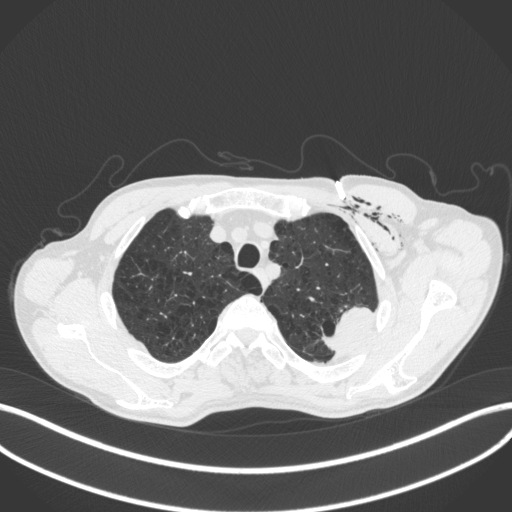
Chest CT, one axial slice. Position 345 of 416 along the scan axis. Reconstruction kernel B31f. 120 kVp. Lung window (W 1500 / L -600 HU). 1 mm slice thickness. 512 × 512 image matrix, field of view 400 × 400 mm. Patient: male, 58 years. From the clinical record (not read from this slice): clinical TNM (as recorded): T3 N0 M0.
Outlined on this slice (bounding box drawn by a radiologist):
- lung tumour (recorded histology: adenocarcinoma): bounding box (x1, y1, x2, y2) in pixels: (314, 300, 373, 360)